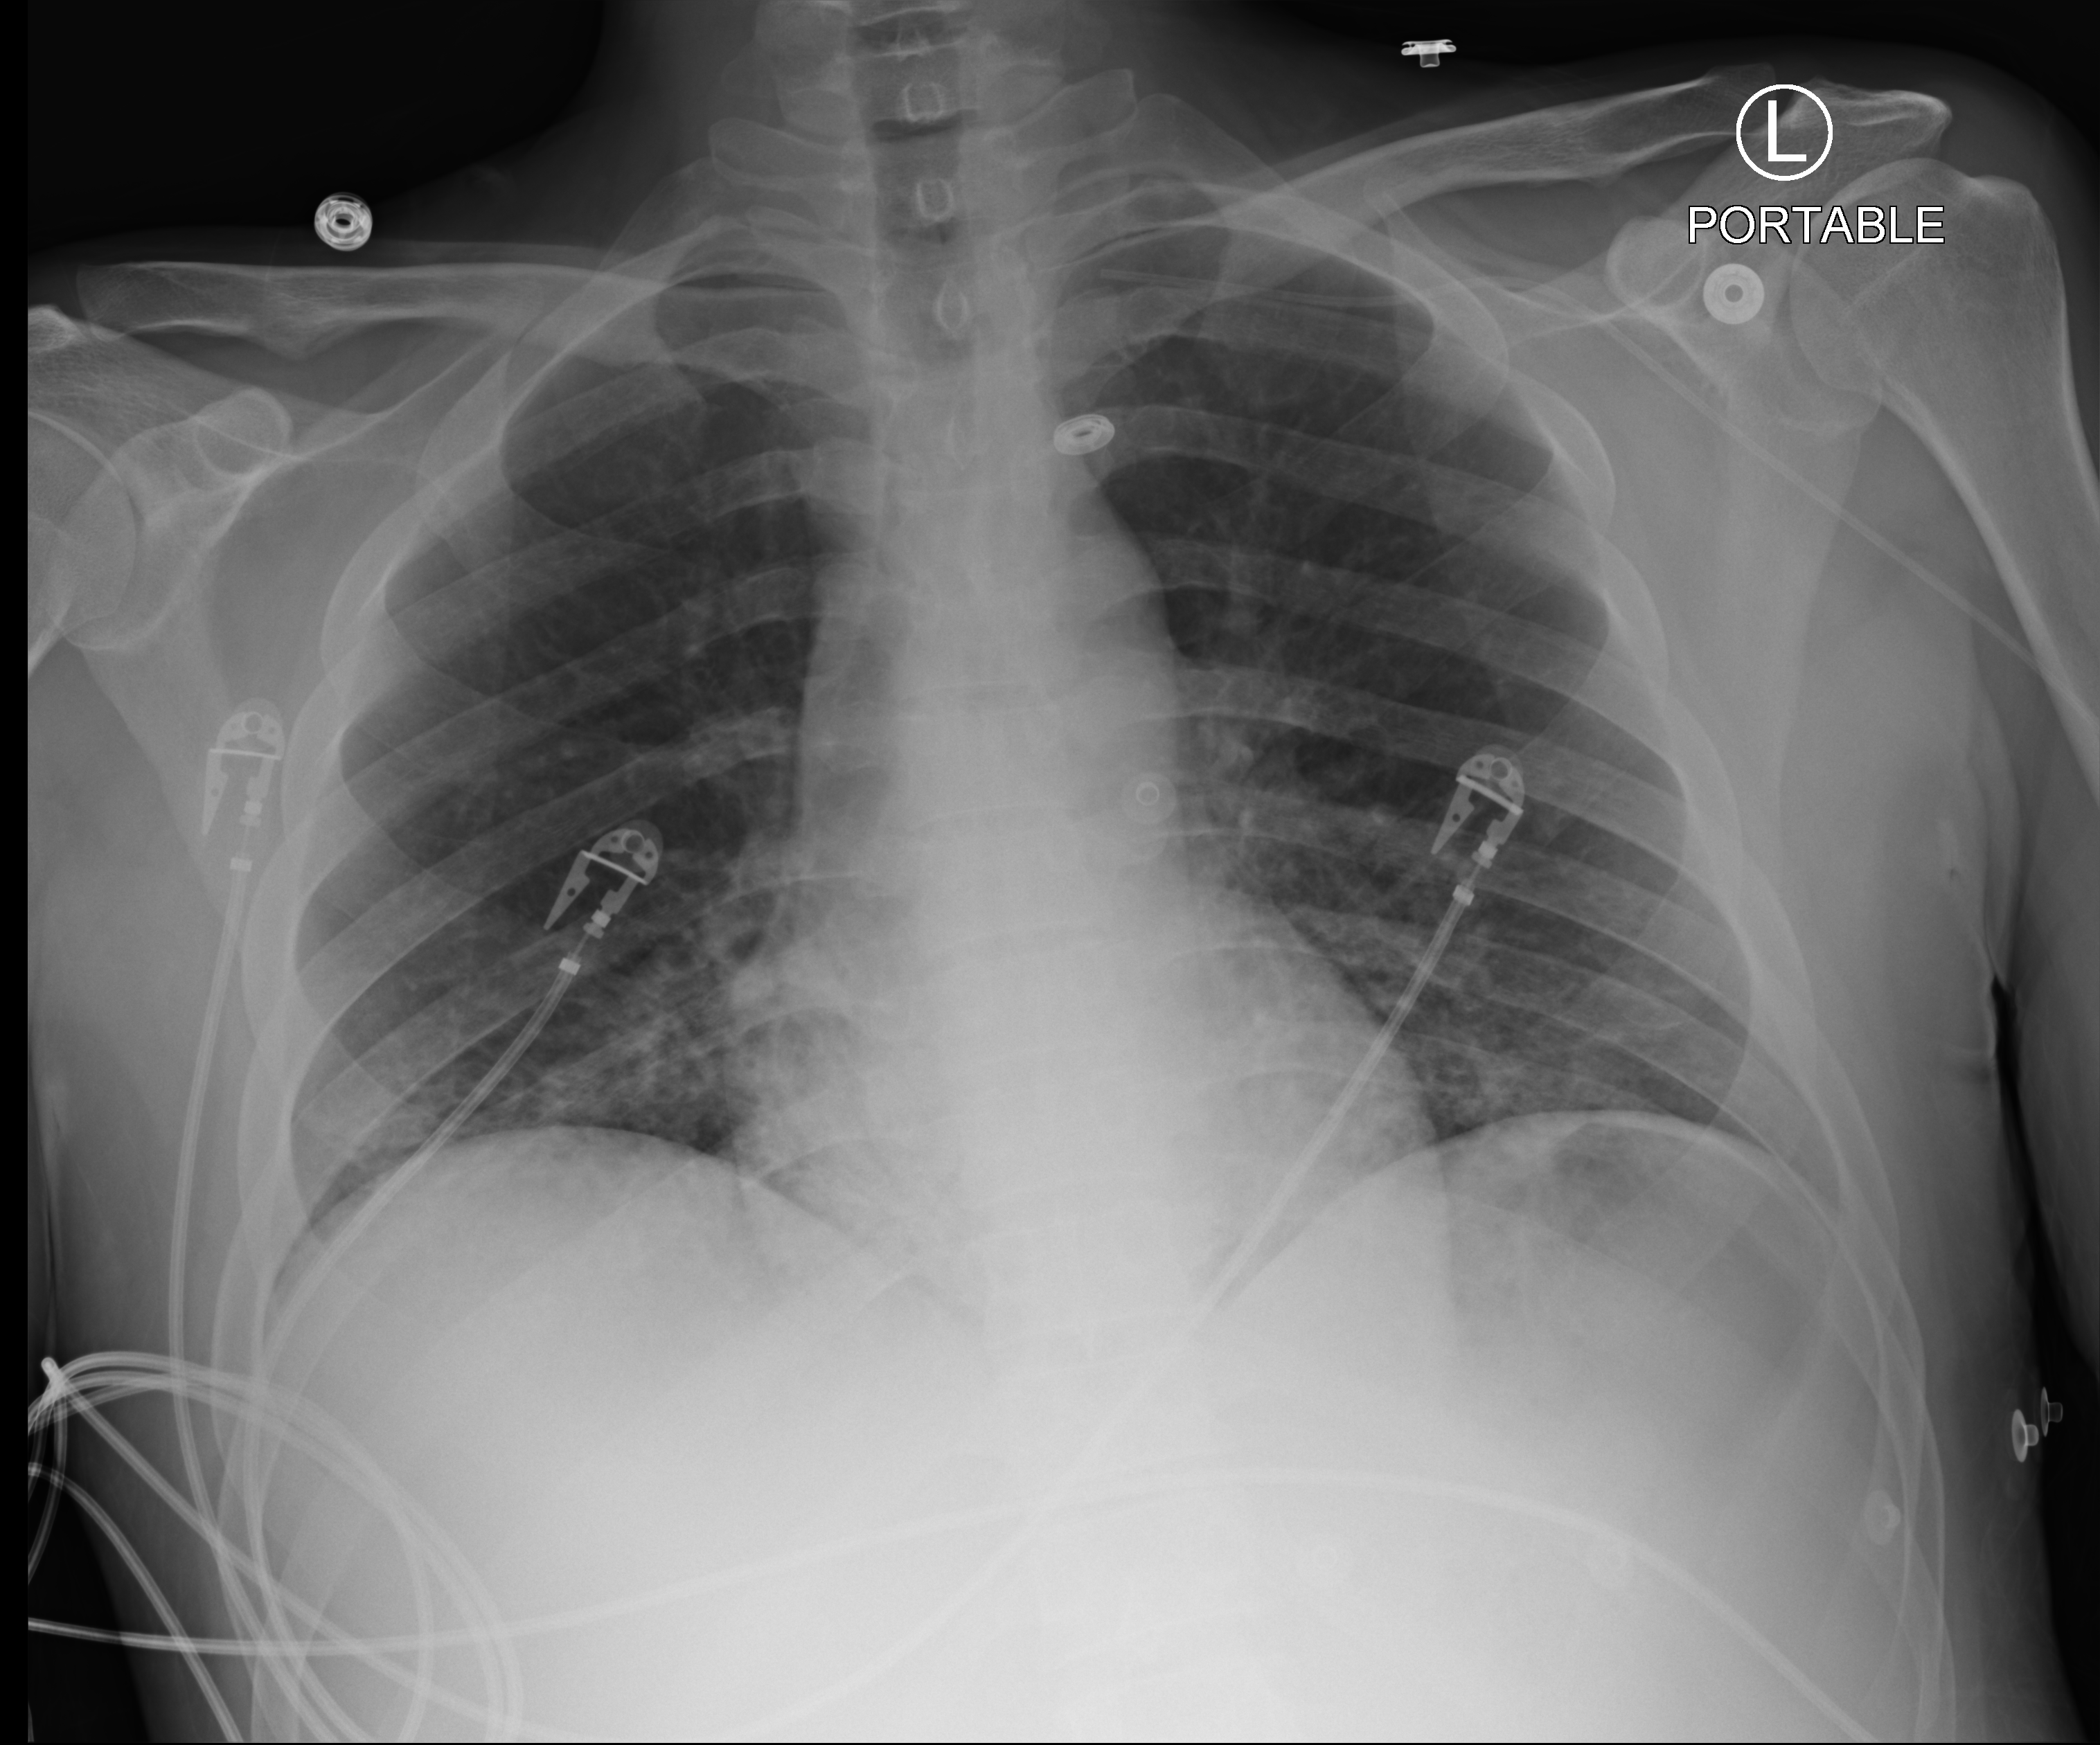
Chest X-ray (portable); anteroposterior (AP) projection. Patient hospitalised with COVID-19; male, aged 18–59 years.
Admission-level facts for this patient (not findings on this image; timing relative to this image not recorded):
- COPD (admission record): no
- admitted to intensive care during this hospital stay: yes
- mechanically ventilated during this hospital stay: yes